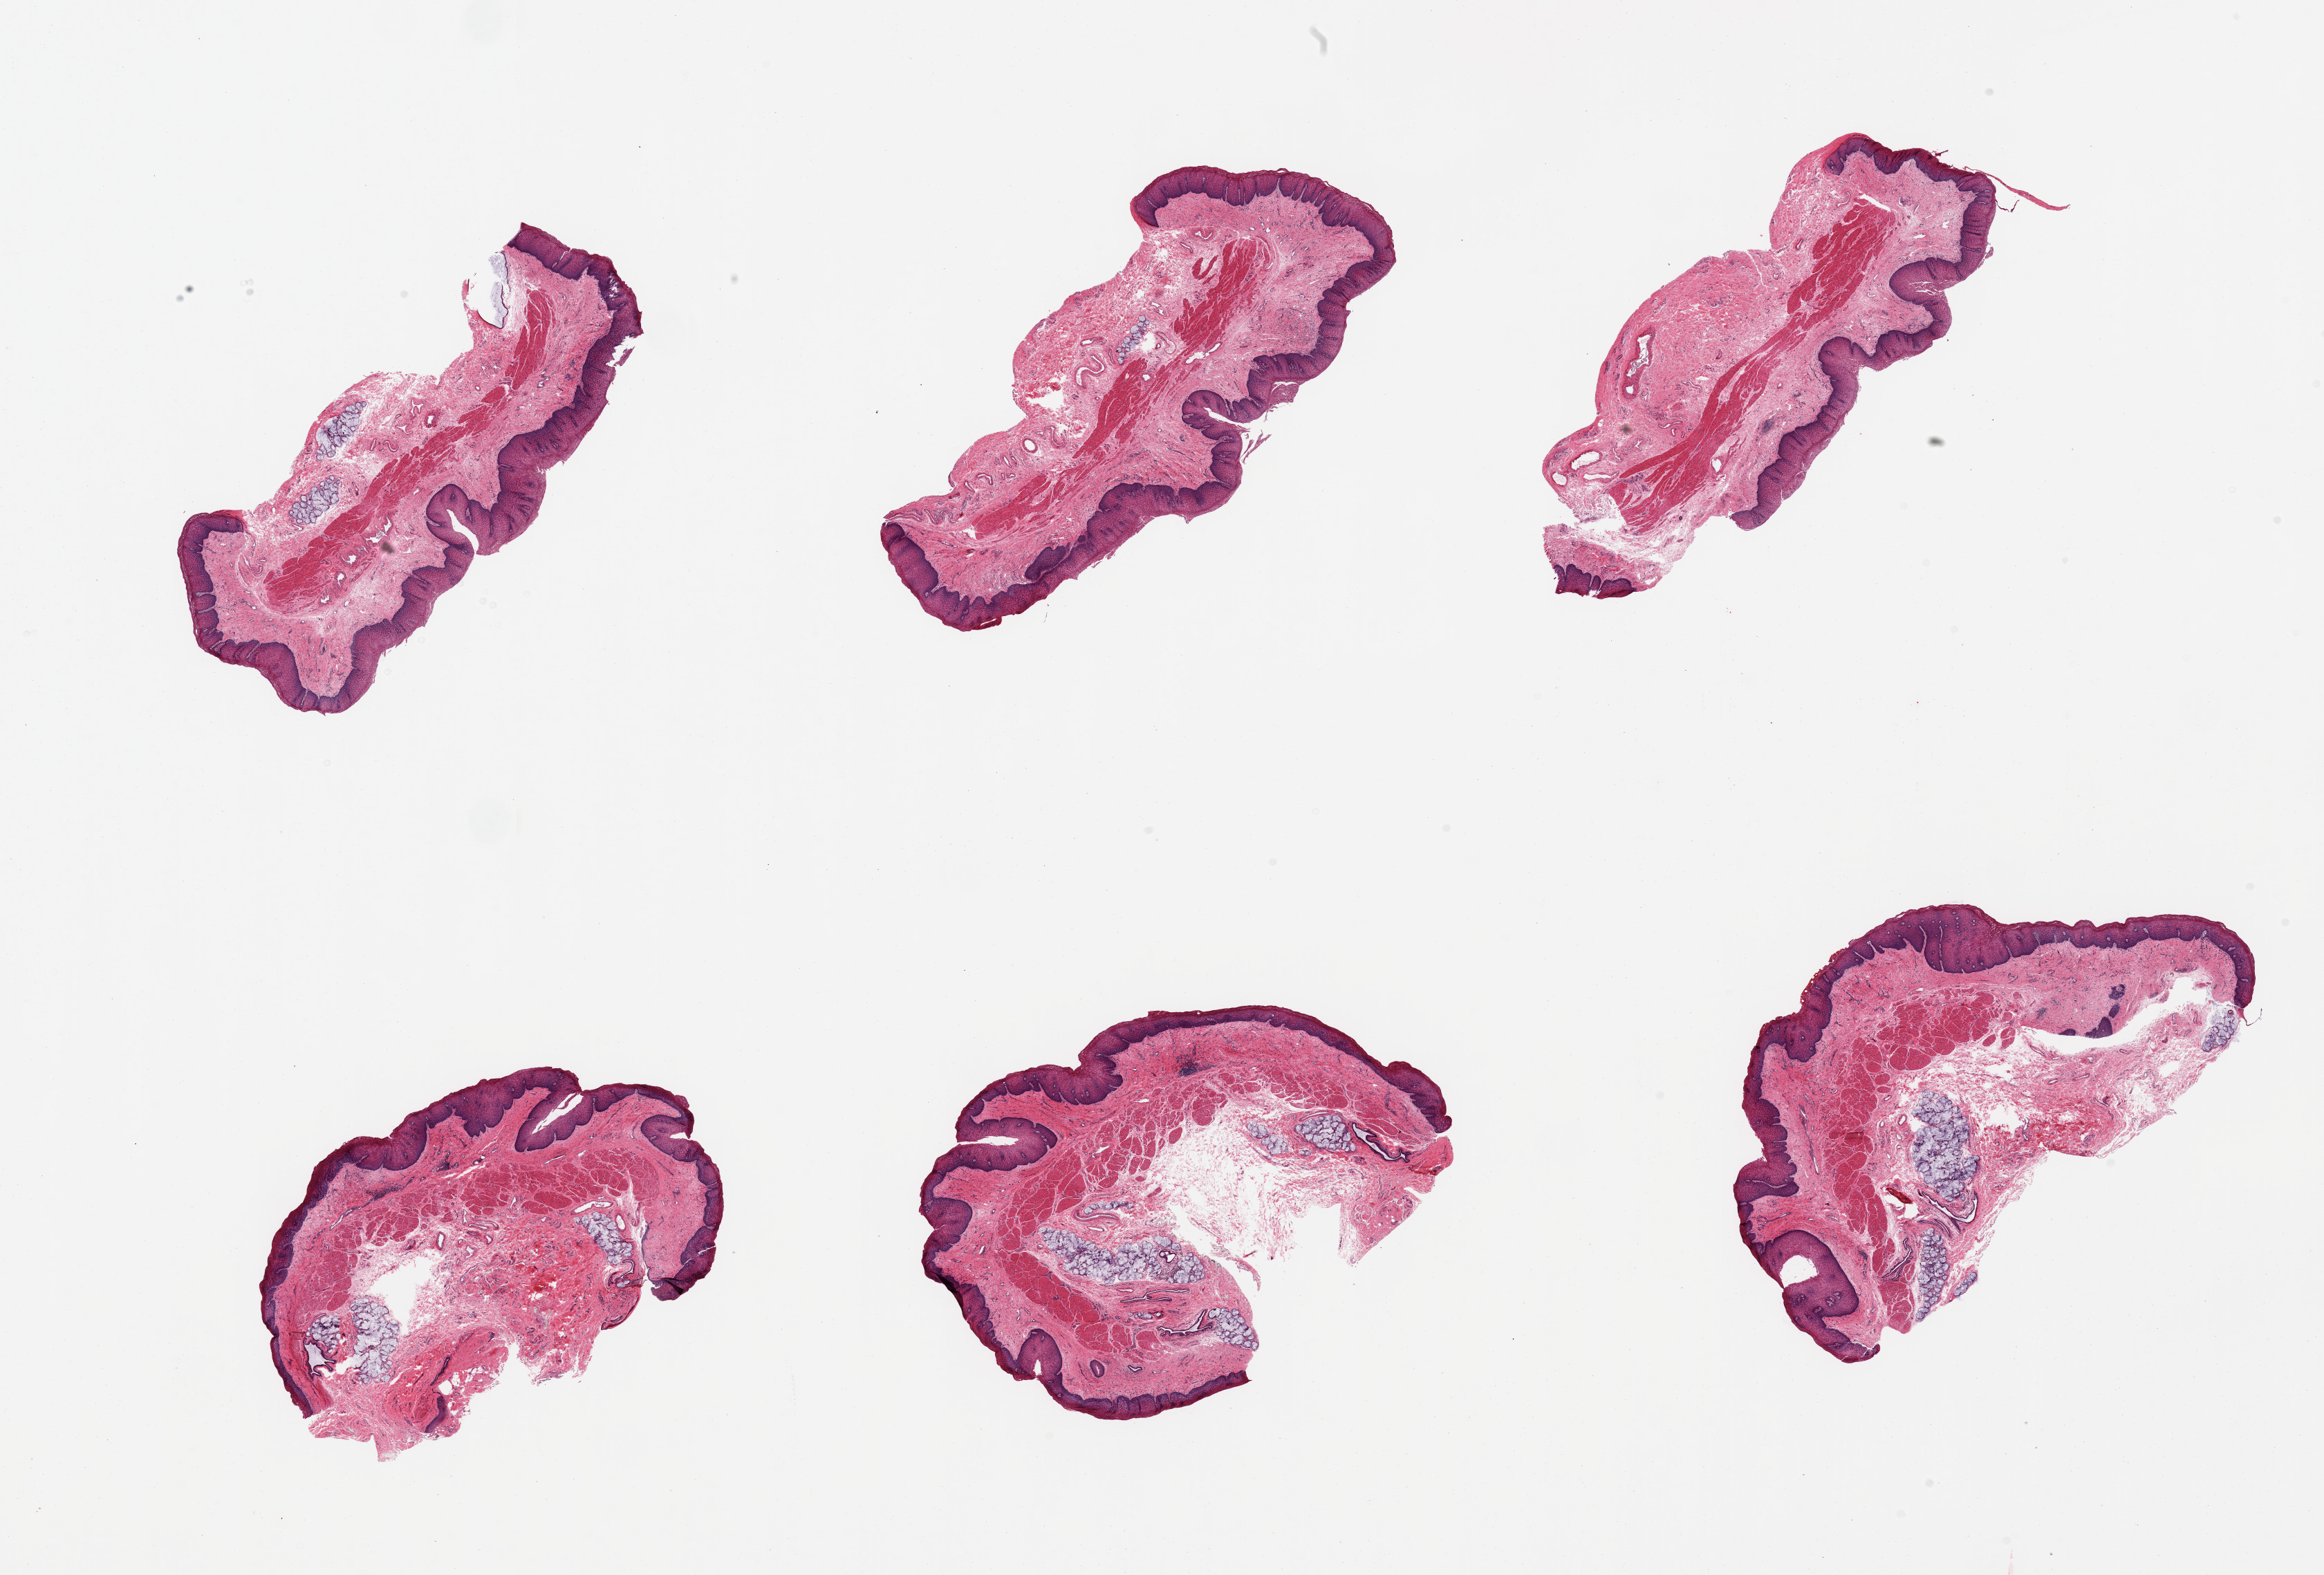
Whole-slide image, haematoxylin and eosin stain — shown as a low-resolution overview of the whole scanned area (about 26.6 x 18.0 mm), PAXgene-fixed paraffin-embedded (PFPE) section, target tissue: esophageal mucous membrane, tissue donor sample. Donor: male.
- pathologist's review note for this sample: 6 pieces; prominent submucosal mucous glands in 4 pieces up to 10% area